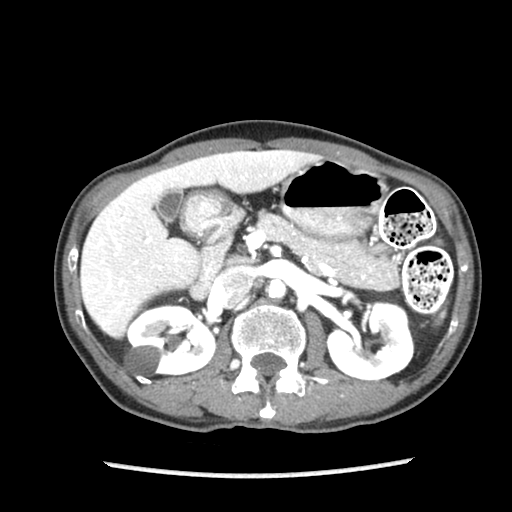
Contrast-enhanced abdominal CT (liver protocol), one axial slice; soft-tissue window (W 400 / L 40 HU); 2.5 mm slice thickness; 512 × 512 image matrix, field of view 300 × 300 mm. From the clinical record (not read from this slice): diagnosis: hepatocellular carcinoma (patient treated with transarterial chemoembolisation; whether this scan precedes or follows treatment is not stated here); TNM stage (as recorded): Stage-IIIB.
Outlined on this slice (semi-automatically segmented with operator editing):
- liver parenchyma outside the tumour (the mass and vessels are separate outlines, so this box may not span the whole liver): box from (x=80, y=150) to (x=321, y=338) px
- liver vessels: (x=94, y=178)–(x=178, y=306)